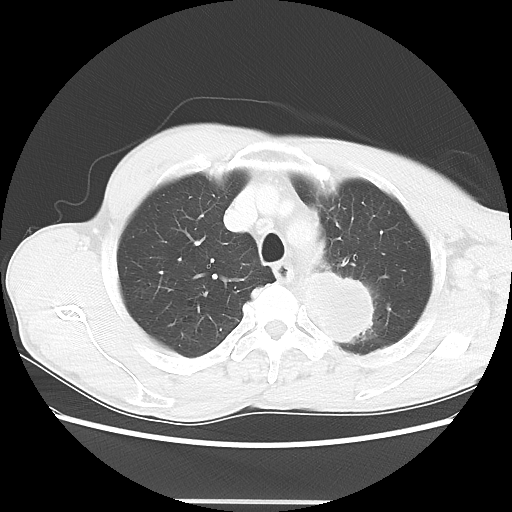
Chest CT, one axial slice; slice 52 of 62 in the series (ordered by position); 100 kVp; lung window (W 1500 / L -600 HU); 512 × 512 image matrix. Patient: male, 61 years. From the clinical record (not read from this slice): clinical TNM (as recorded): T3 N1 M1.
Structures marked on this image (rectangle marked by the reading radiologist):
- lung tumour (recorded histology: adenocarcinoma): bounding box [x1, y1, x2, y2] px = [302, 269, 382, 350]